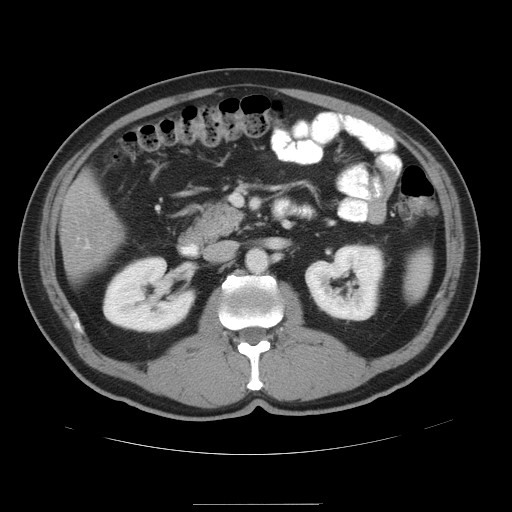
Contrast-enhanced abdominal CT, one axial slice. Position 20 of 47 along the scan axis. Intravenous contrast given. Soft-tissue window (W 400 / L 40 HU). 512 × 512 image matrix, field of view 420 × 420 mm. Male patient, age 61 years. From the clinical record (not read from this slice): diagnosis: colorectal cancer liver metastases, imaged before liver resection; multiple liver metastases: no; largest metastasis: 1.2 cm; disease in both lobes: no.
Outlined on this slice (manually delineated by an expert):
- hepatic veins: bounding box [x1, y1, x2, y2] px = [86, 242, 90, 248]
- liver: [62, 176, 122, 277]
- planned liver remnant (the part of the liver to remain after resection): [66, 176, 122, 249]